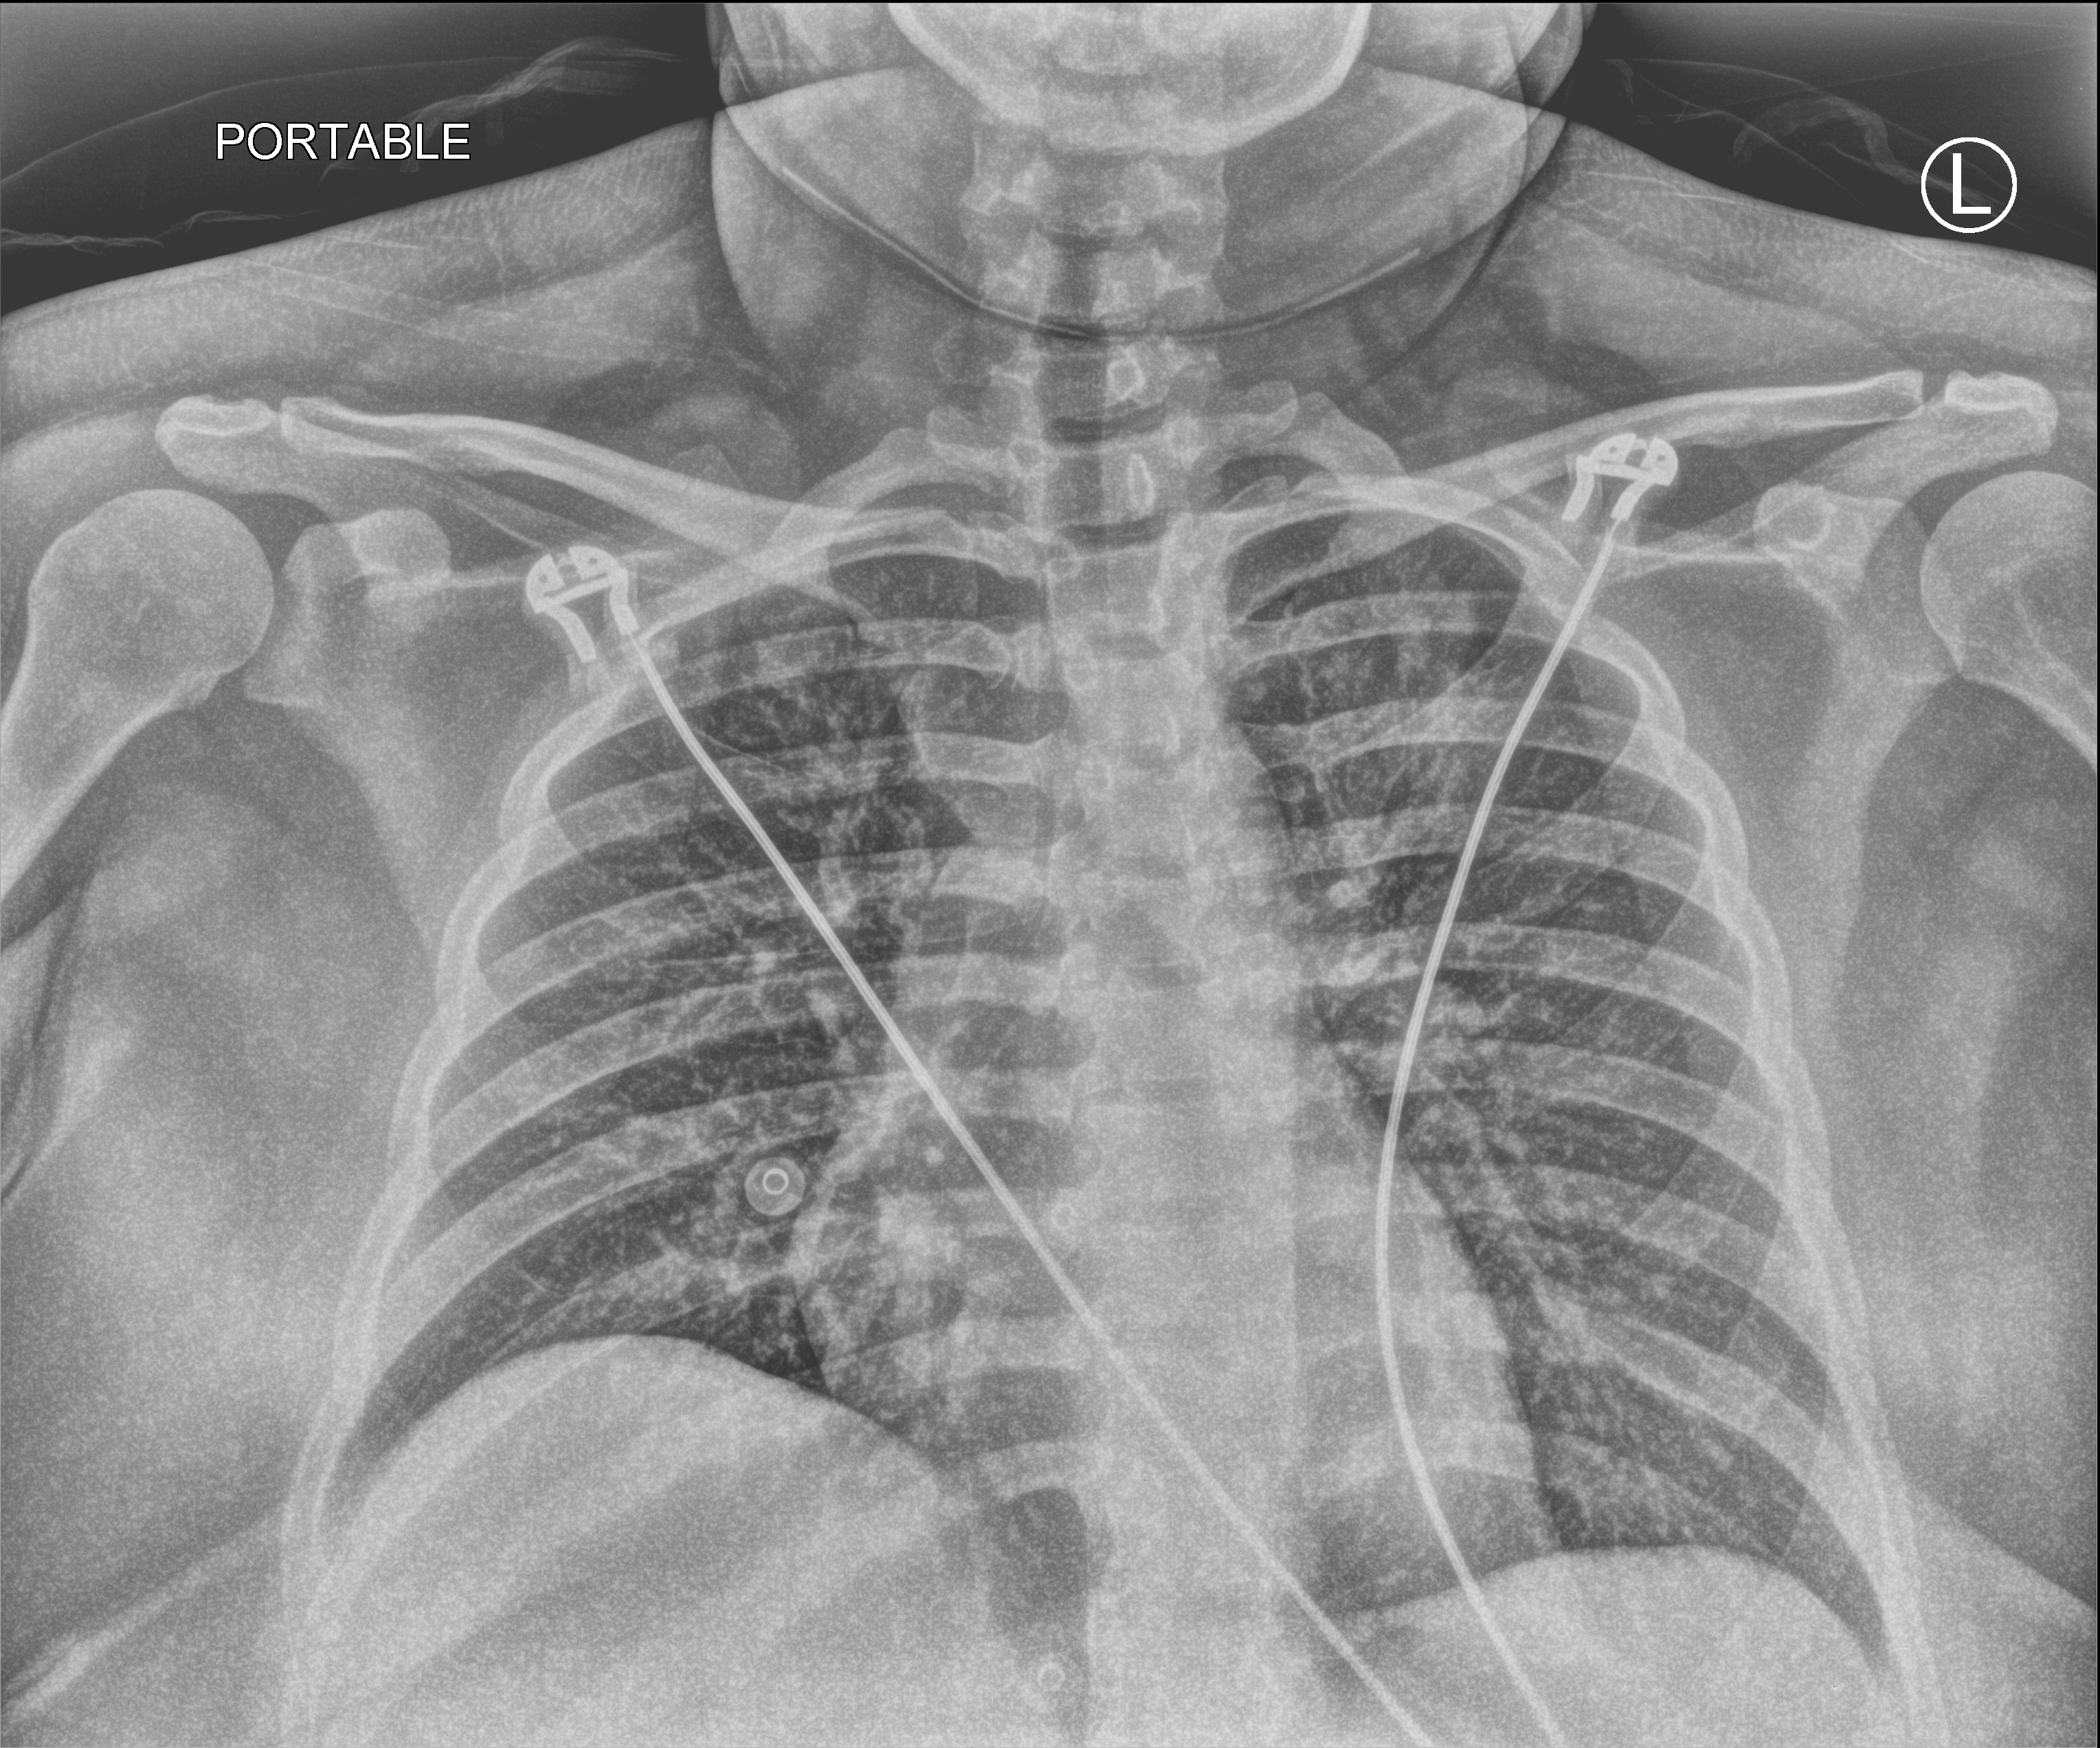
Portable chest radiograph. Female patient hospitalised with COVID-19, age 18–59 years.
Admission-level facts for this patient (not findings on this image; timing relative to this image not recorded): smoking status (admission record): never; length of hospital stay: 1 day; admitted to intensive care during this hospital stay: no.